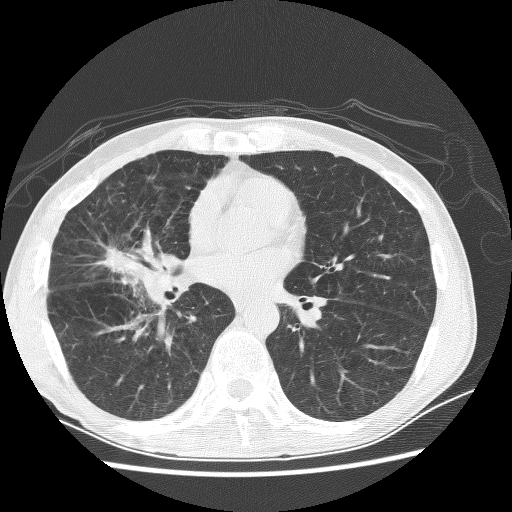
Chest CT (low-dose screening protocol), one axial image. Baseline screening round. Lung window (W 1500 / L -600 HU). 2.5 mm slice thickness. 512 × 512 image matrix. Male, age 67 years at enrolment.
Expert-annotated lung lesion, bounding box [x1, y1, x2, y2] px = [76, 225, 172, 298]. Screening reader's record for this exam (one nodule recorded; not confirmed to be the boxed lesion): non-calcified nodule or mass ≥4 mm, right middle lobe, 28 × 18 mm, spiculated (stellate) margins, soft tissue attenuation. Official screen result: positive, change unspecified: nodule(s) >= 4 mm or enlarging nodule(s), mass(es), or other non-specific abnormalities suspicious for lung cancer. Later outcome: lung cancer diagnosed 69 days after this screen — adenocarcinoma, NOS, right middle lobe, stage IV (AJCC 6th edition), 60 mm at pathology.